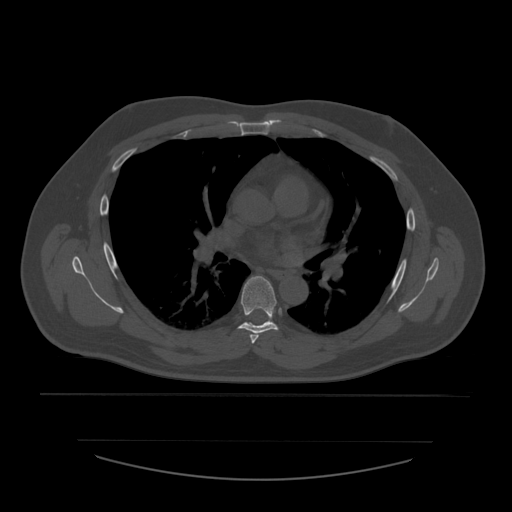
CT including the spine, one axial slice. Position 380 of 532 along the scan axis. Reconstruction kernel STANDARD. 120 kVp. Bone window (W 1800 / L 400 HU). 512 × 512 image matrix, field of view 441 × 441 mm. Patient age 44 years. Case-level facts recorded for this patient, not image findings: primary cancer: soft tissue sarcoma.
Structures marked on this image (semi-automatically segmented with operator editing):
- T5 vertebra: bounding box (x1, y1, x2, y2) in pixels: (250, 333, 259, 344)
- T6 vertebra: (238, 276, 279, 334)